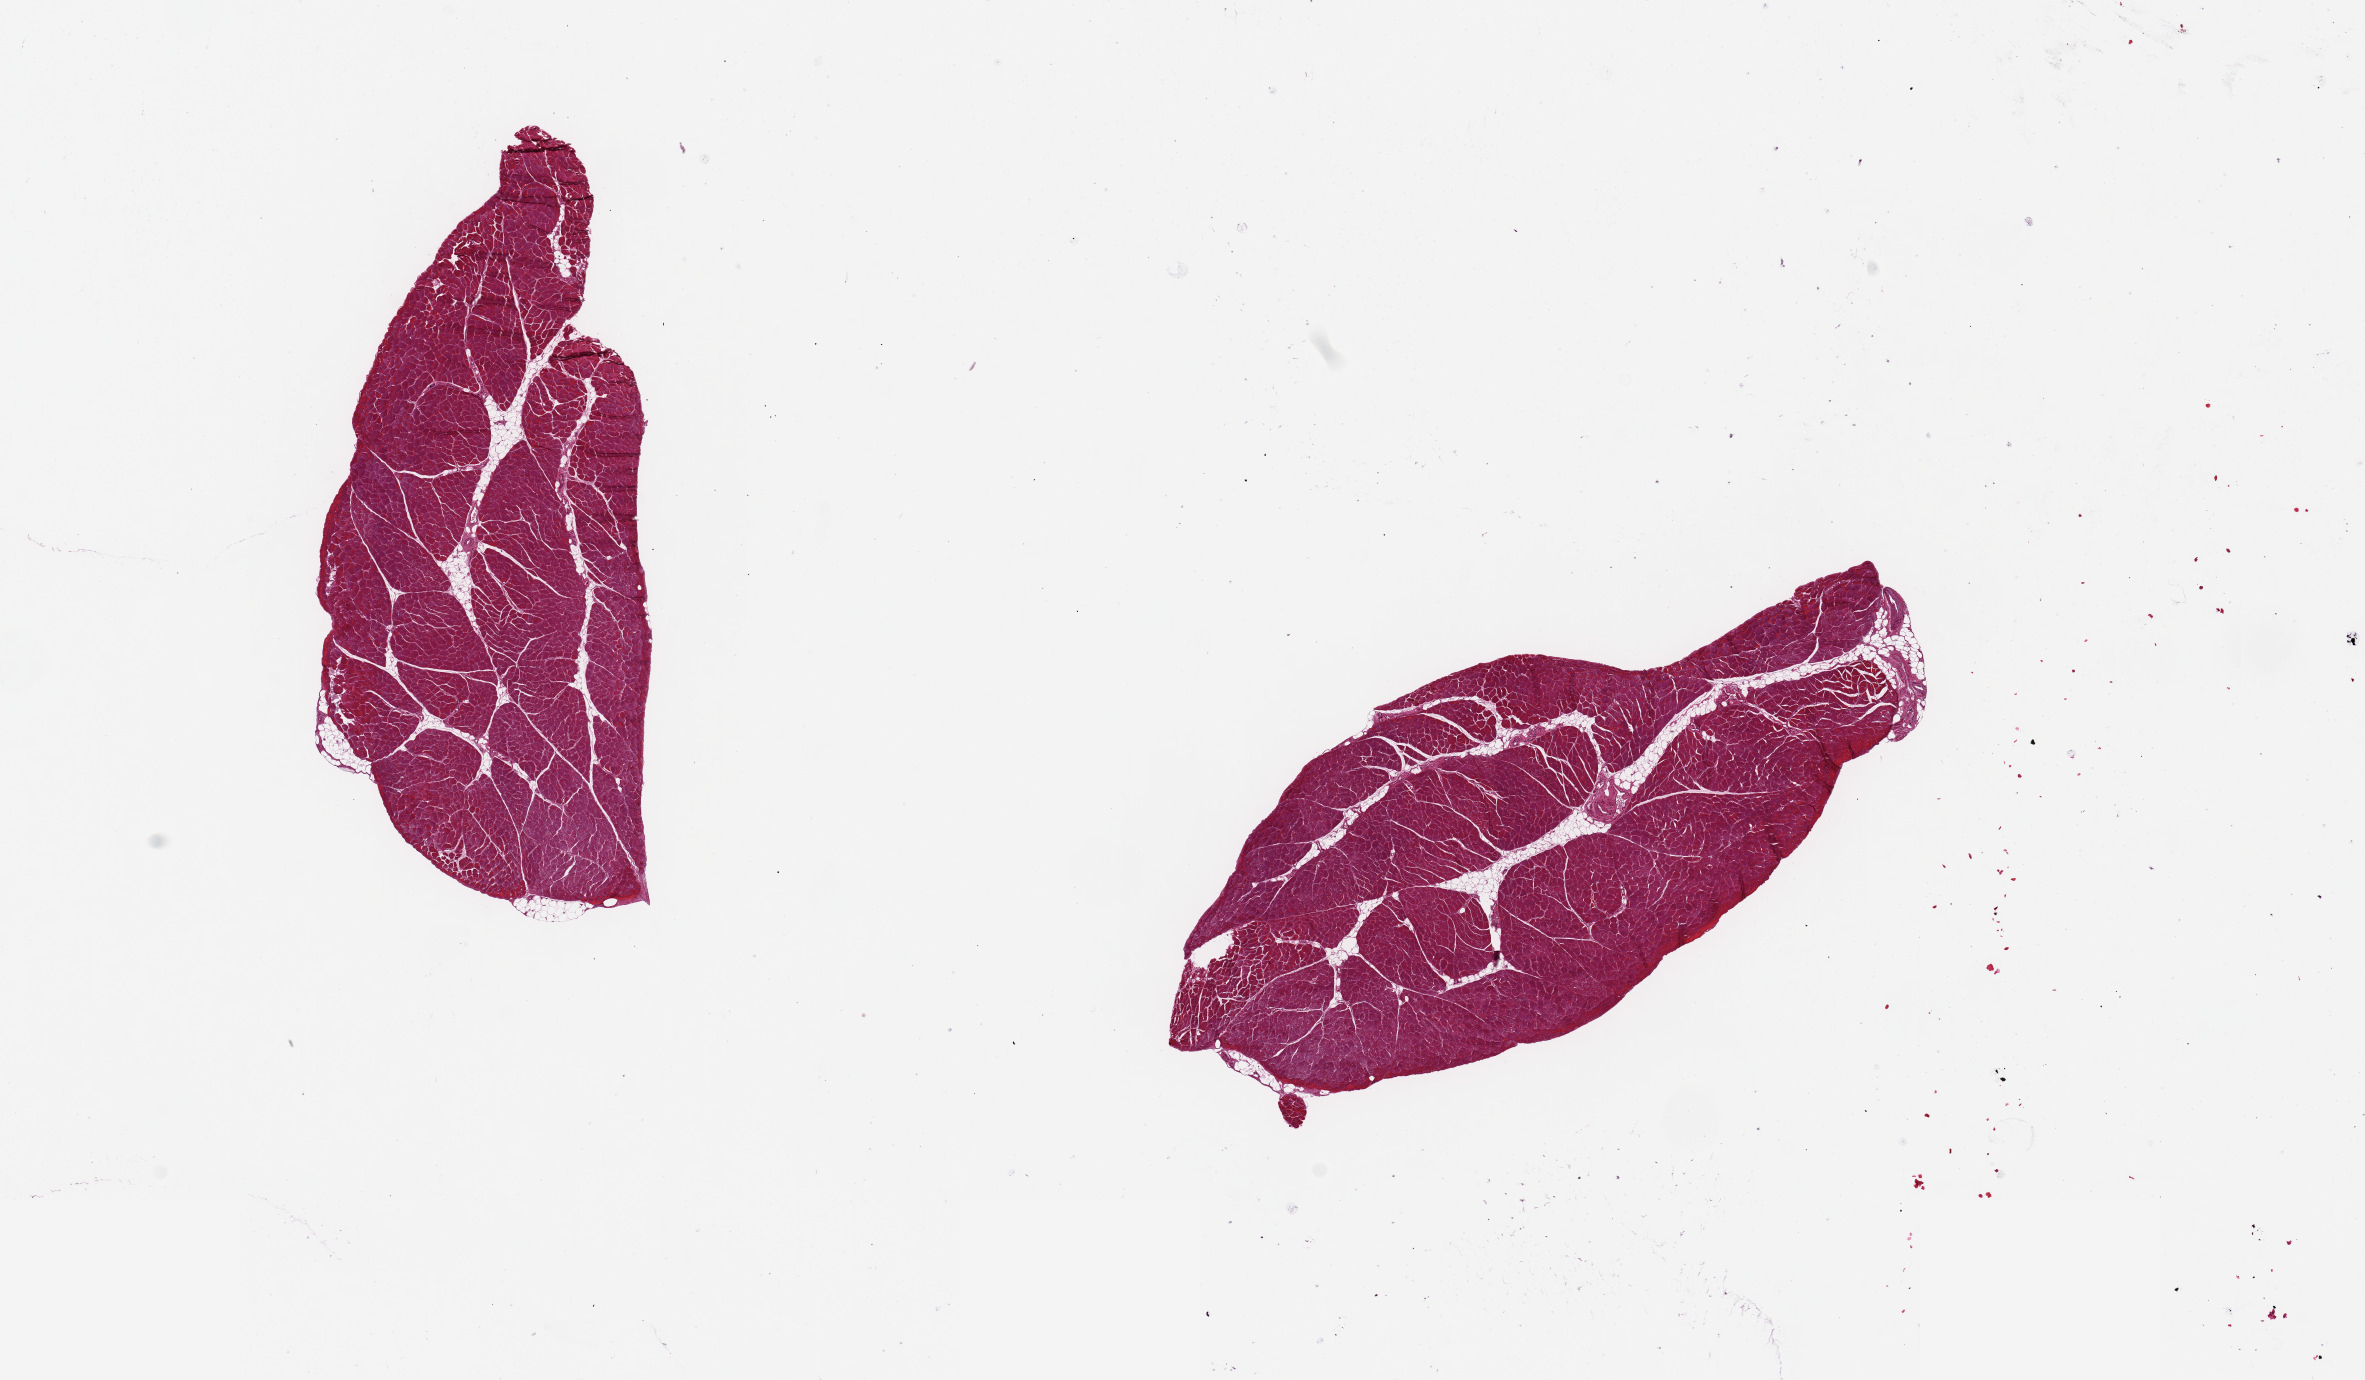
Whole-slide image, H&E stain, brightfield, low-resolution overview of the scanned area, about 18.7 x 10.9 mm (from a 20x scan); PAXgene-fixed paraffin-embedded (PFPE) section; section of skeletal muscle (target tissue); donor tissue sample. Donor sex: male.
Review note (as recorded): 2 pieces ~6x3mm, ~10% interstitial fat.